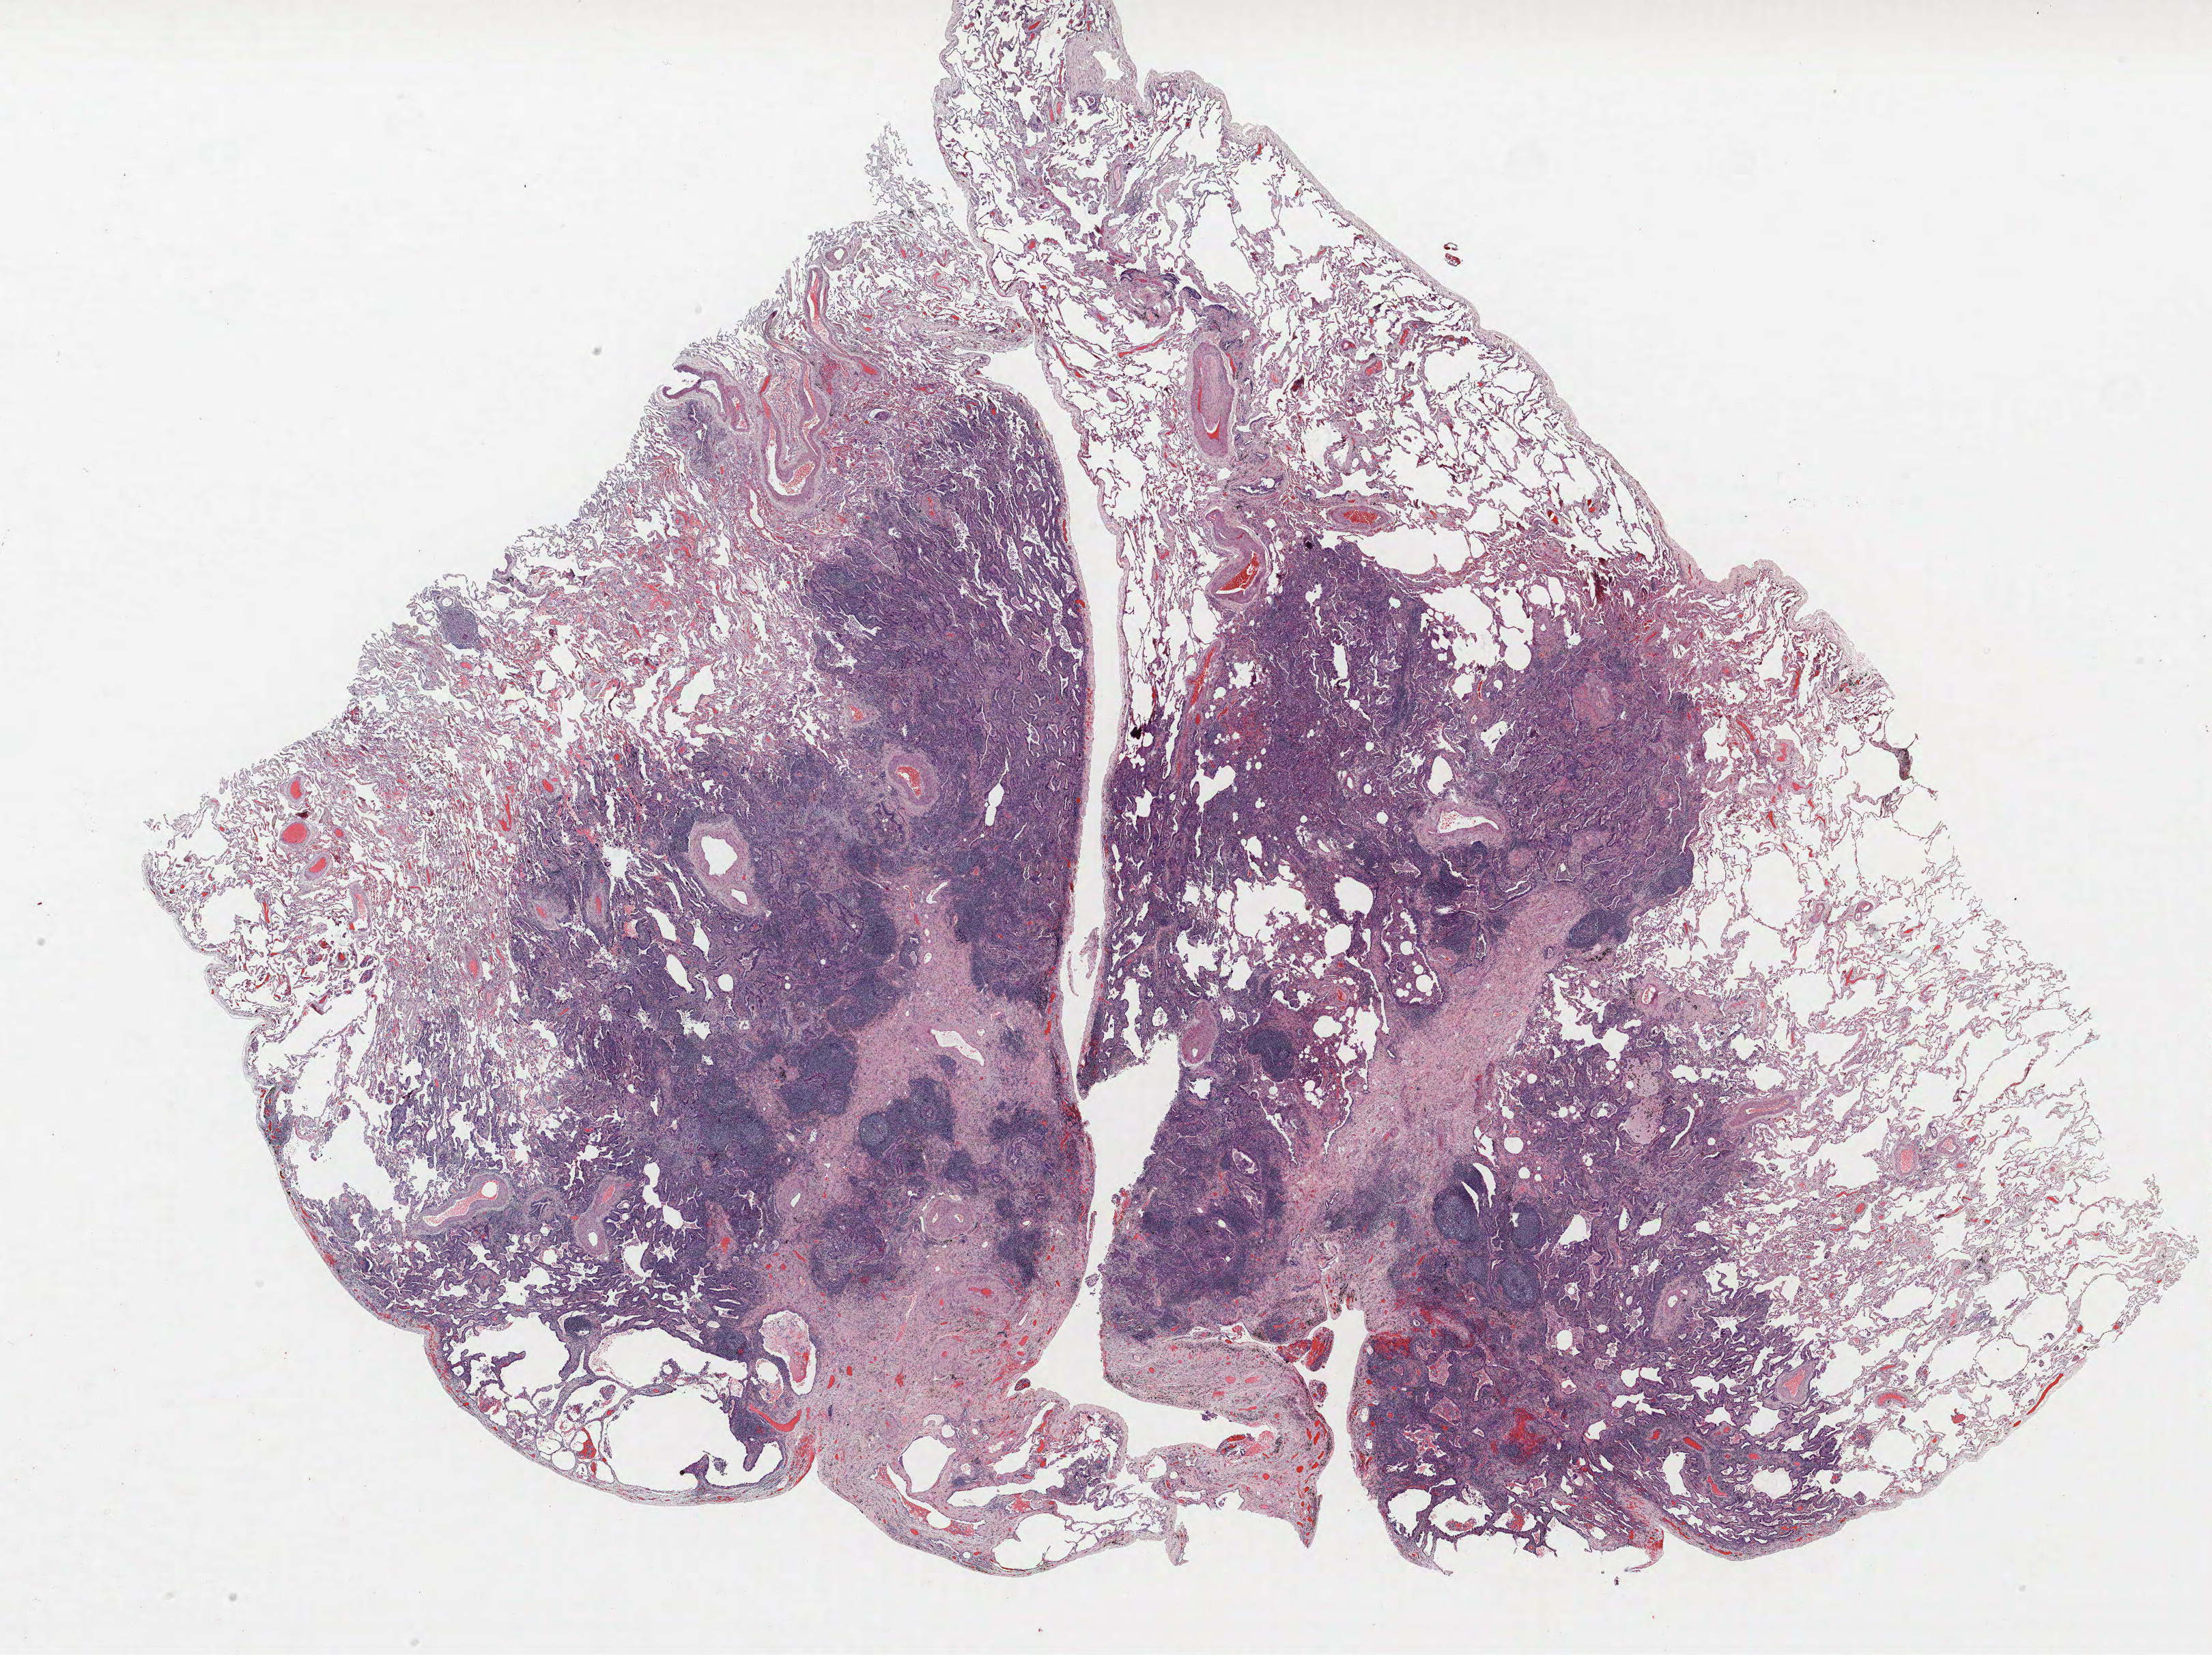
Hematoxylin and eosin (H&E) stained whole-slide image, whole scanned area (about 25.9 x 19.4 mm, acquisition: 40x scan) shown as a low-resolution overview; FFPE section; lung tissue. Female patient, aged 64 at enrolment. Grade: moderately differentiated (G2).
- participant's lung-cancer diagnosis: Adenocarcinoma, NOS (ICD-O-3 8140/3)
- tumour size (pathology): 15 mm
- primary tumour location (clinical record): right lower lobe
- stage (AJCC 6th edition): IA